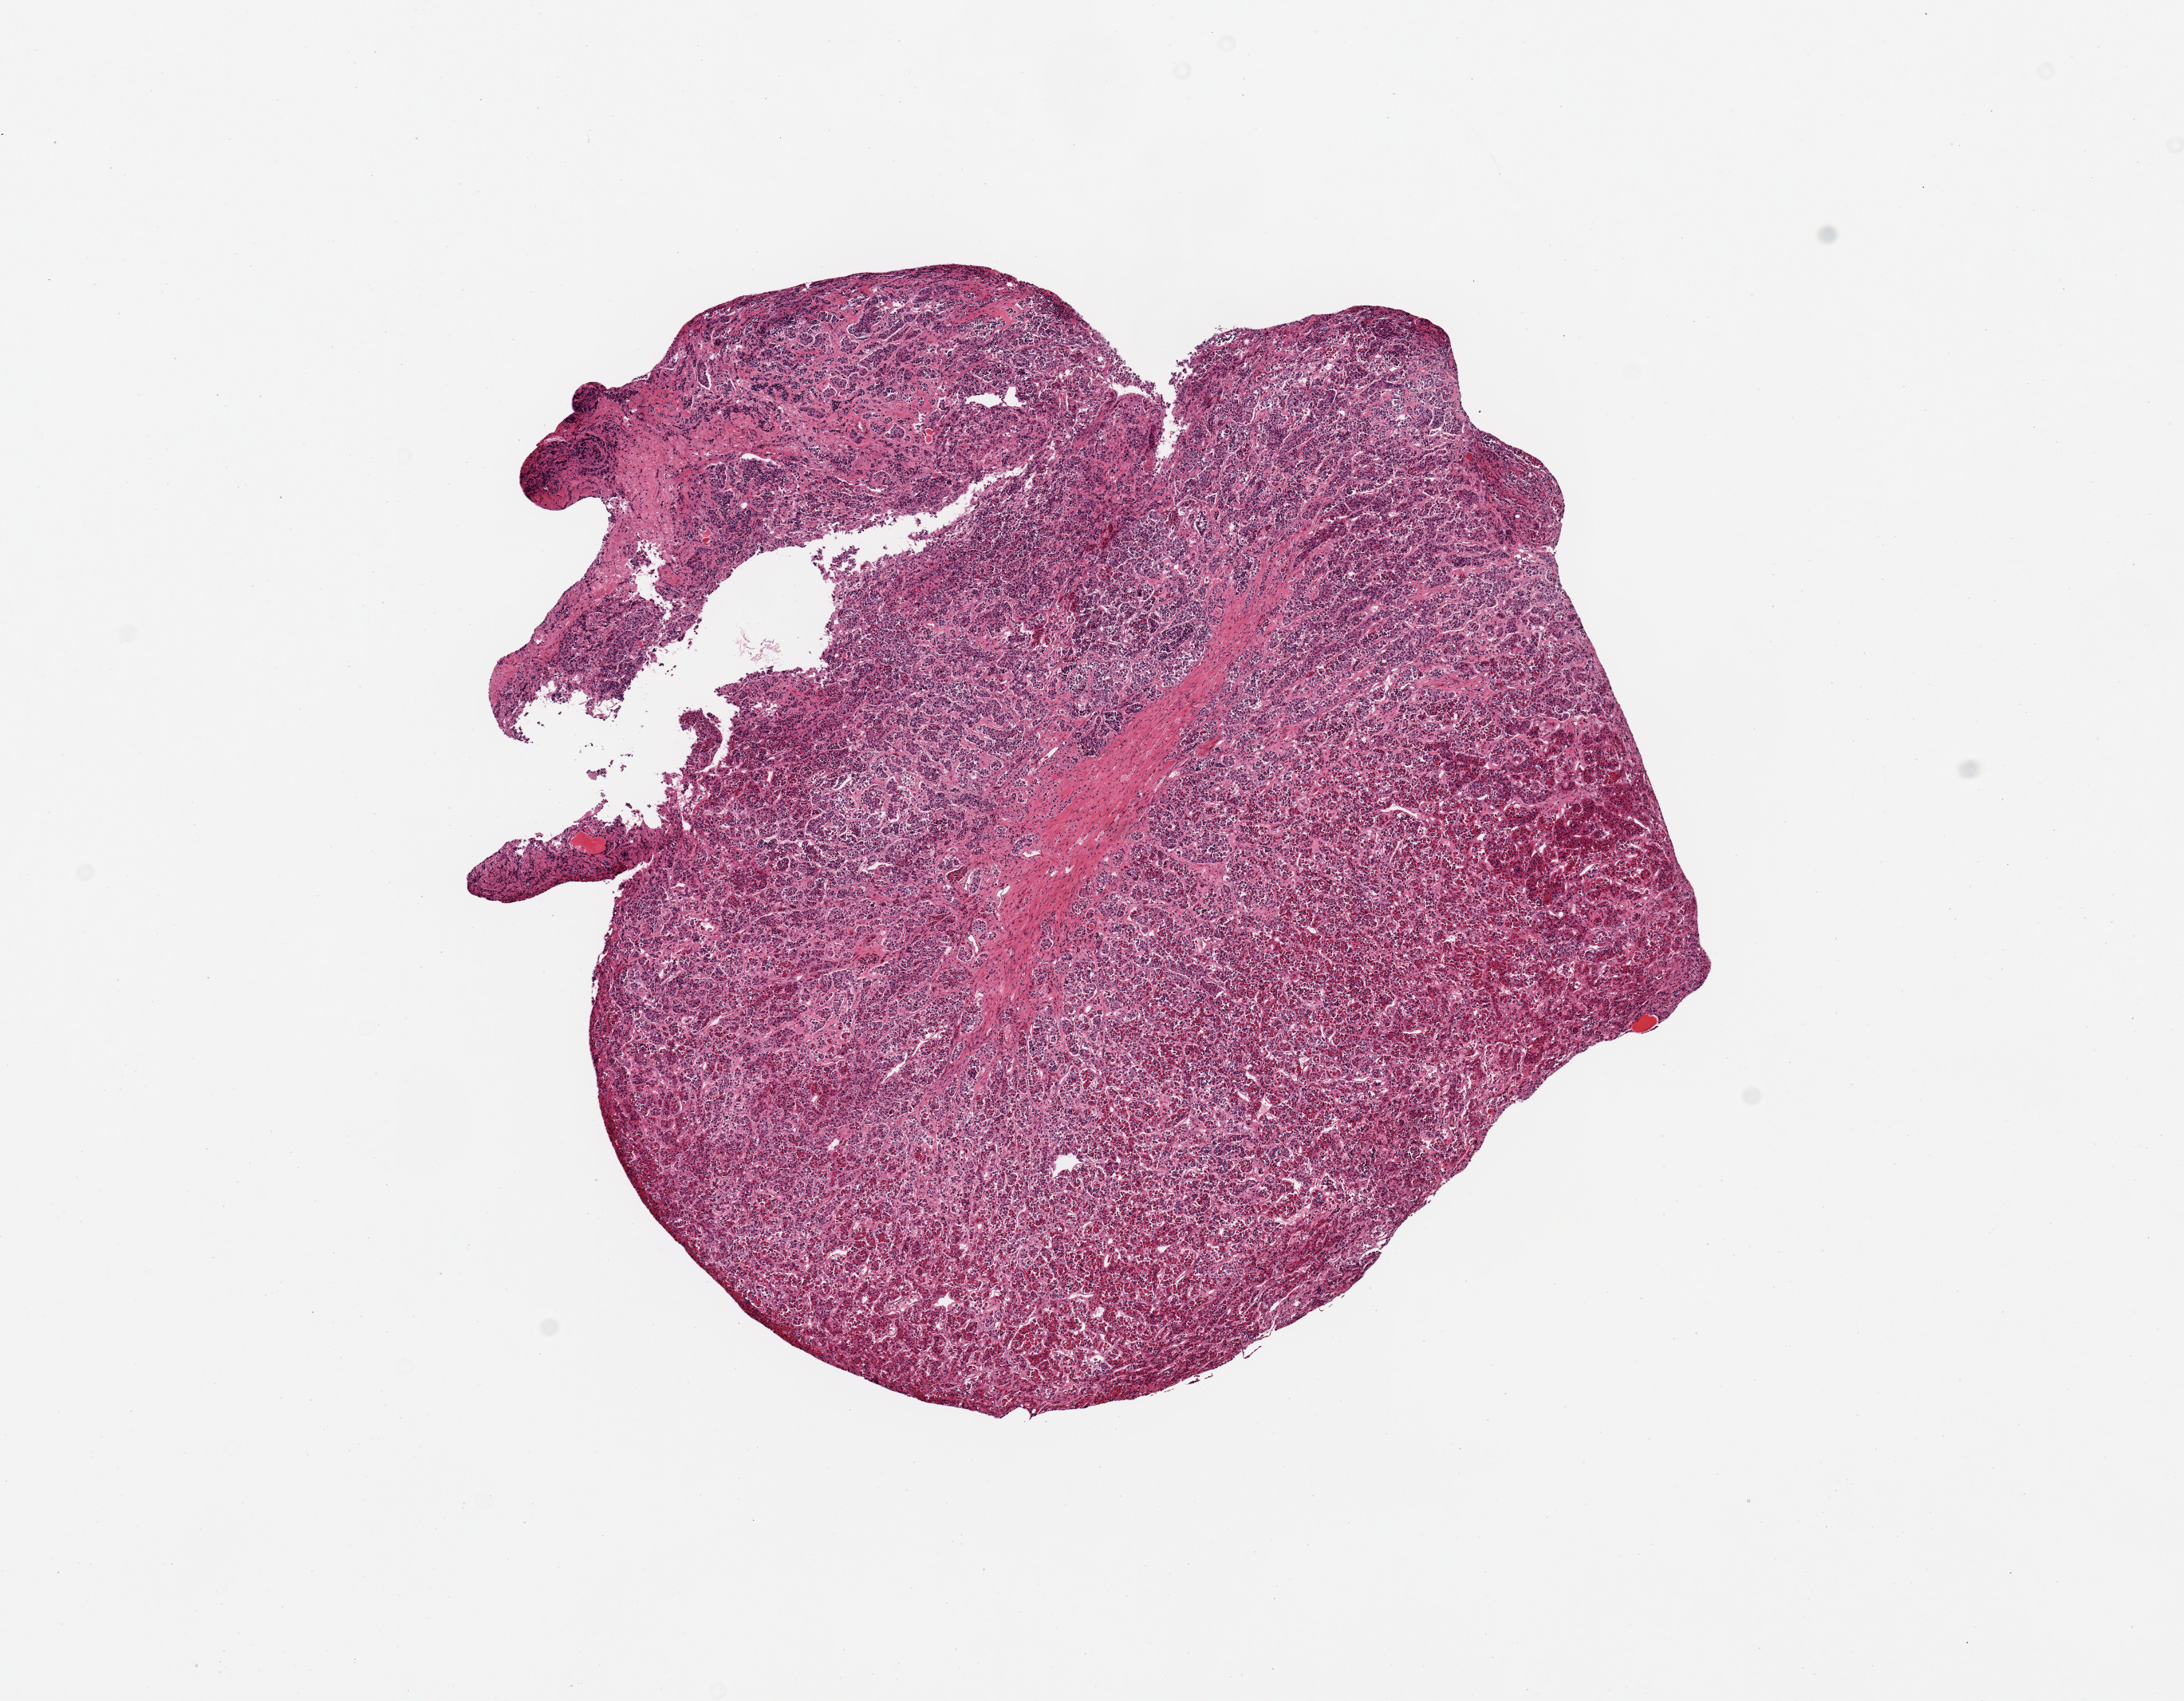
Haematoxylin and eosin whole-slide image, brightfield — a low-resolution overview of the entire scanned area, about 10.8 x 8.4 mm. PAXgene-fixed paraffin-embedded (PFPE) section. Target tissue: pituitary. Donor tissue sample. Donor sex: male.
Review note (as recorded): 1 piece; mostly adenohypophysis.